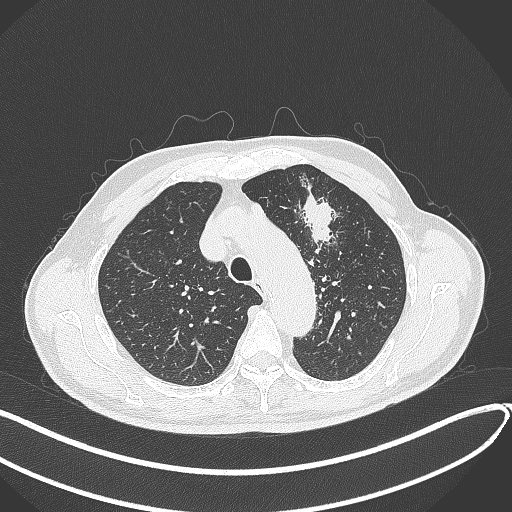
Chest CT, one axial slice. Position 319 of 459 along the scan axis. 120 kVp. Lung window (W 1500 / L -600 HU). 512 × 512 image matrix. Male patient, age 74 years. Case-level facts recorded for this patient, not image findings: clinical TNM (as recorded): T2b N0 M1c.
Structures marked on this image (rectangle marked by the reading radiologist):
- lung tumour (recorded histology: adenocarcinoma): bounding box <298,187,344,252> (left, top, right, bottom; pixels)